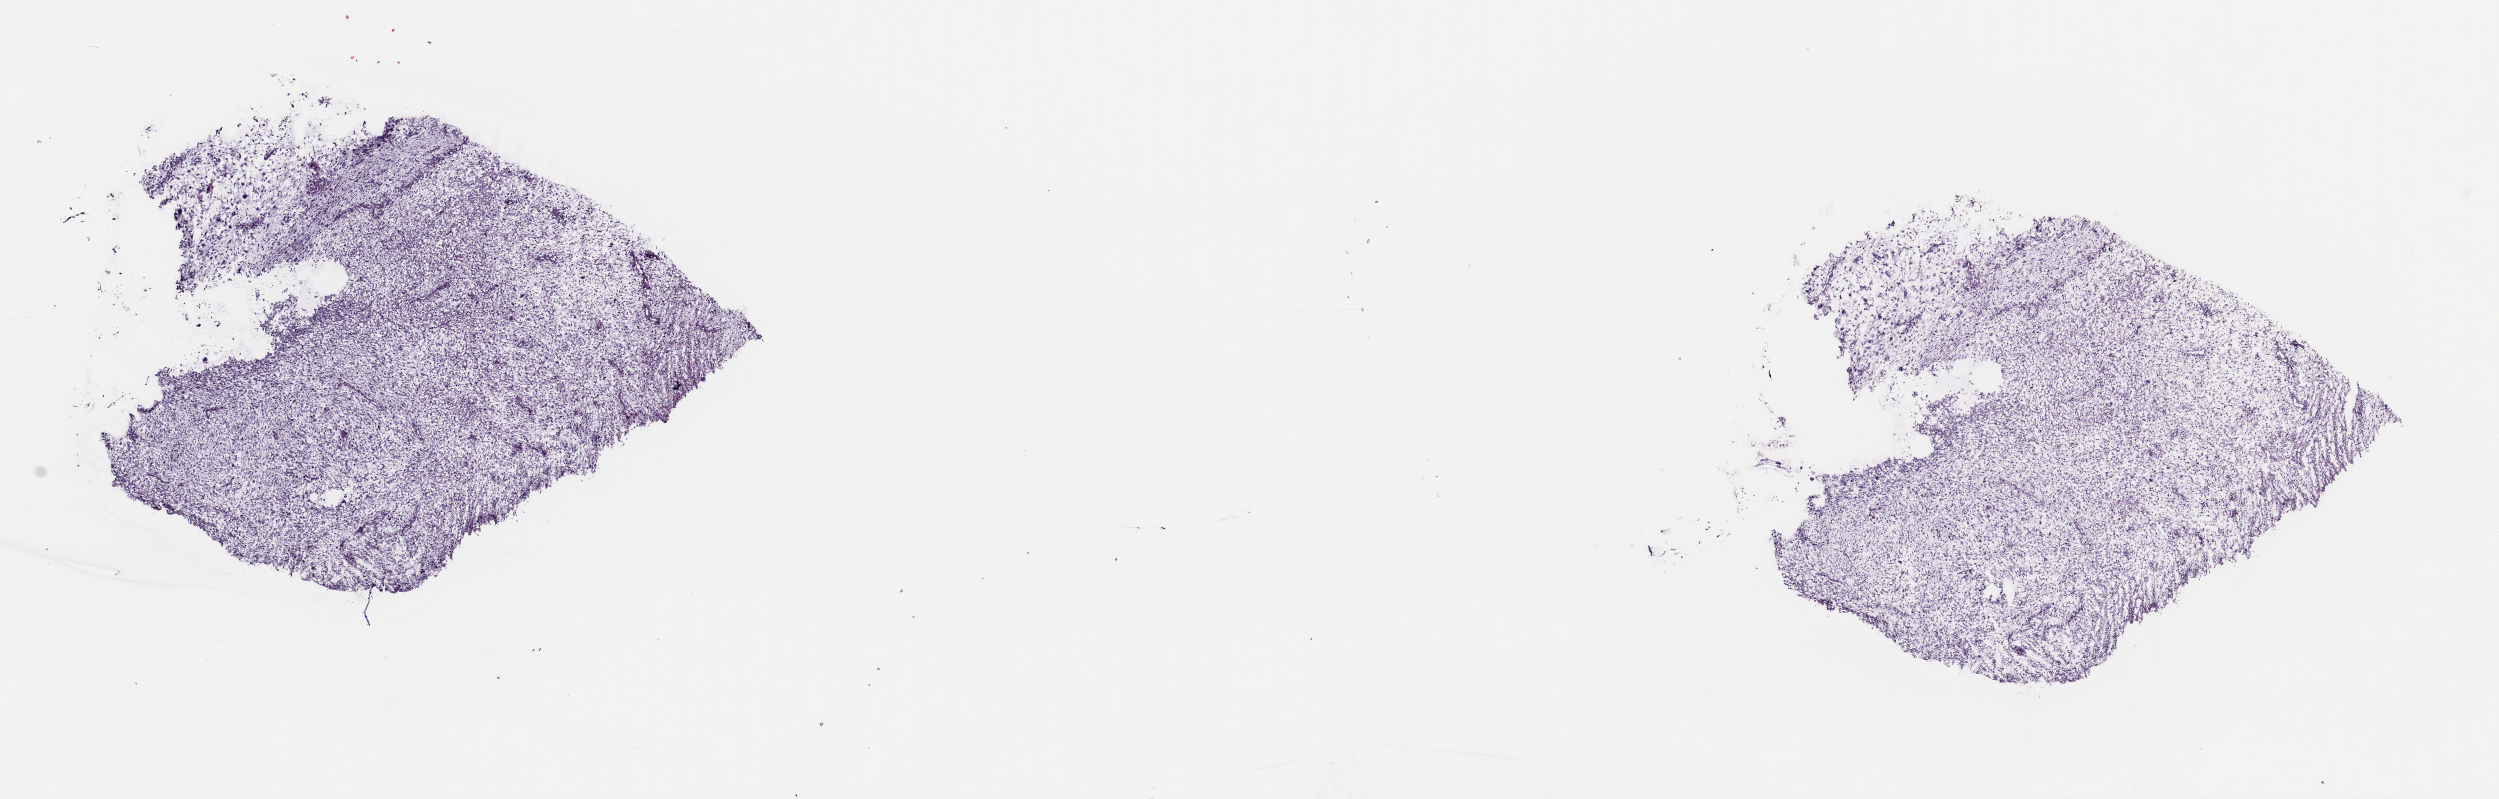
Whole-slide histology image, Hematoxylin and eosin (H&E) stained — a low-resolution overview of the entire scanned area, about 19.7 x 6.3 mm (acquisition: 40x scan). Frozen section from the top of the tissue portion. Primary tumour sample from the connective, subcutaneous and other soft tissues. Patient: female, age at initial diagnosis 65 years. Slide review estimates, as recorded: tumour cells 98%, tumour nuclei 80%, normal cells 0%, stromal cells 0%, necrosis 2%. Inflammatory infiltration, as recorded: lymphocyte infiltration 2%, monocyte infiltration 0%, neutrophil infiltration 0%.
Histologic diagnosis: Undifferentiated sarcoma.